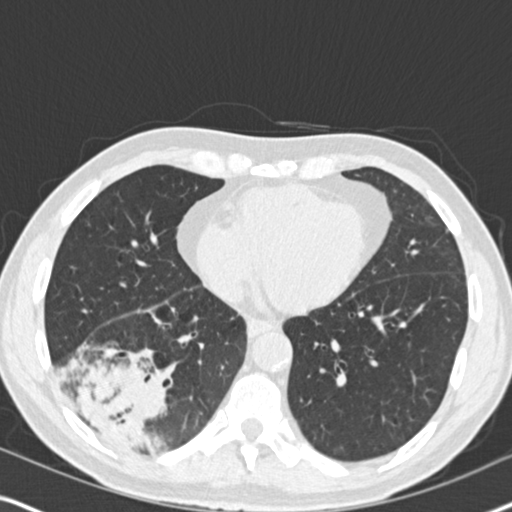
Low-dose screening chest CT, one axial slice. Slice 74 of 182 in the series (ordered by position). Lung window (W 1500 / L -600 HU). 2 mm slice thickness. 512 × 512 image matrix, field of view 330 × 330 mm.
Structures marked on this image (expert manual segmentation):
- lesion 1 (tumor, lower lobe of right lung): bounding box (x1, y1, x2, y2) in pixels: (70, 349, 166, 453)